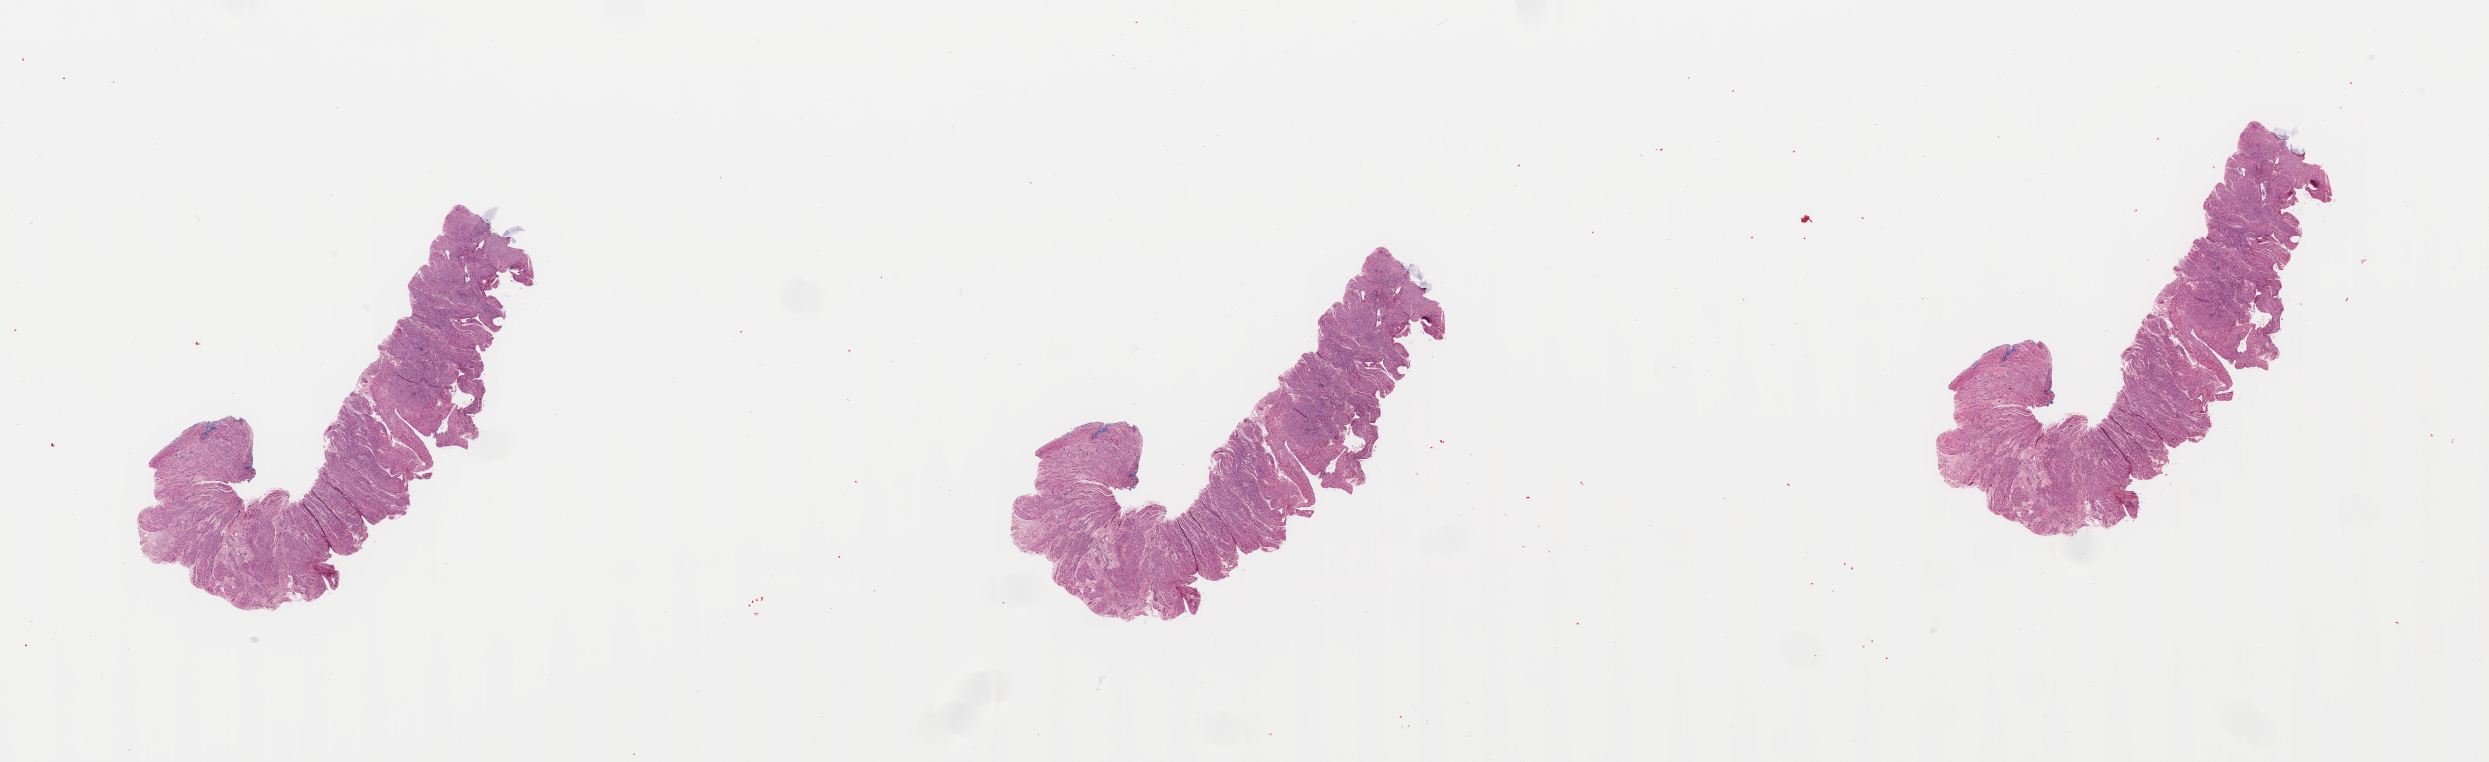
Whole-slide histology image, Hematoxylin and eosin (H&E) stained — low-resolution overview of the scanned area, about 39.4 x 12.1 mm; uterus, normal (non-tumour) tissue. Female, 72 y/o.
* this section: normal (non-tumour) tissue from the same patient
* patient diagnosis: Endometrioid adenocarcinoma, NOS